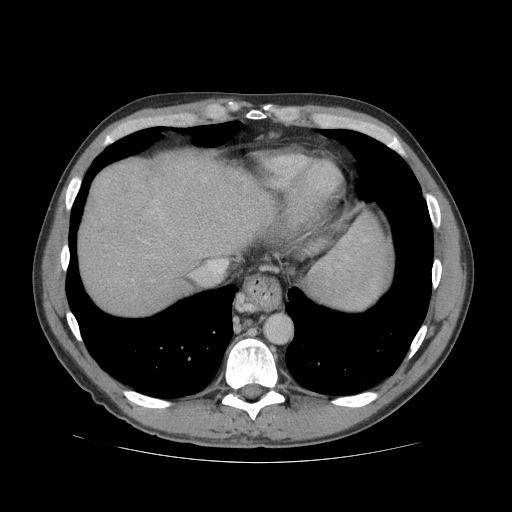
Contrast-enhanced abdominal CT (liver protocol), one axial slice. Position 66 of 81 along the scan axis. Reconstruction kernel STANDARD. 140 kVp. Soft-tissue window (W 400 / L 40 HU). 2.5 mm slice thickness. 512 × 512 image matrix. From the clinical record (not read from this slice): diagnosis: hepatocellular carcinoma (patient treated with transarterial chemoembolisation; whether this scan precedes or follows treatment is not stated here); TNM stage (as recorded): Stage-IVB; Child-Pugh class: B; tumour nodularity: multinodular.
Structures marked on this image (semi-automatically segmented with operator editing):
- liver parenchyma outside the tumour (the mass and vessels are separate outlines, so this box may not span the whole liver): bounding box (x1, y1, x2, y2) in pixels: (78, 154, 276, 314)
- mass: (90, 160, 151, 234)
- liver vessels: (144, 209, 162, 243)